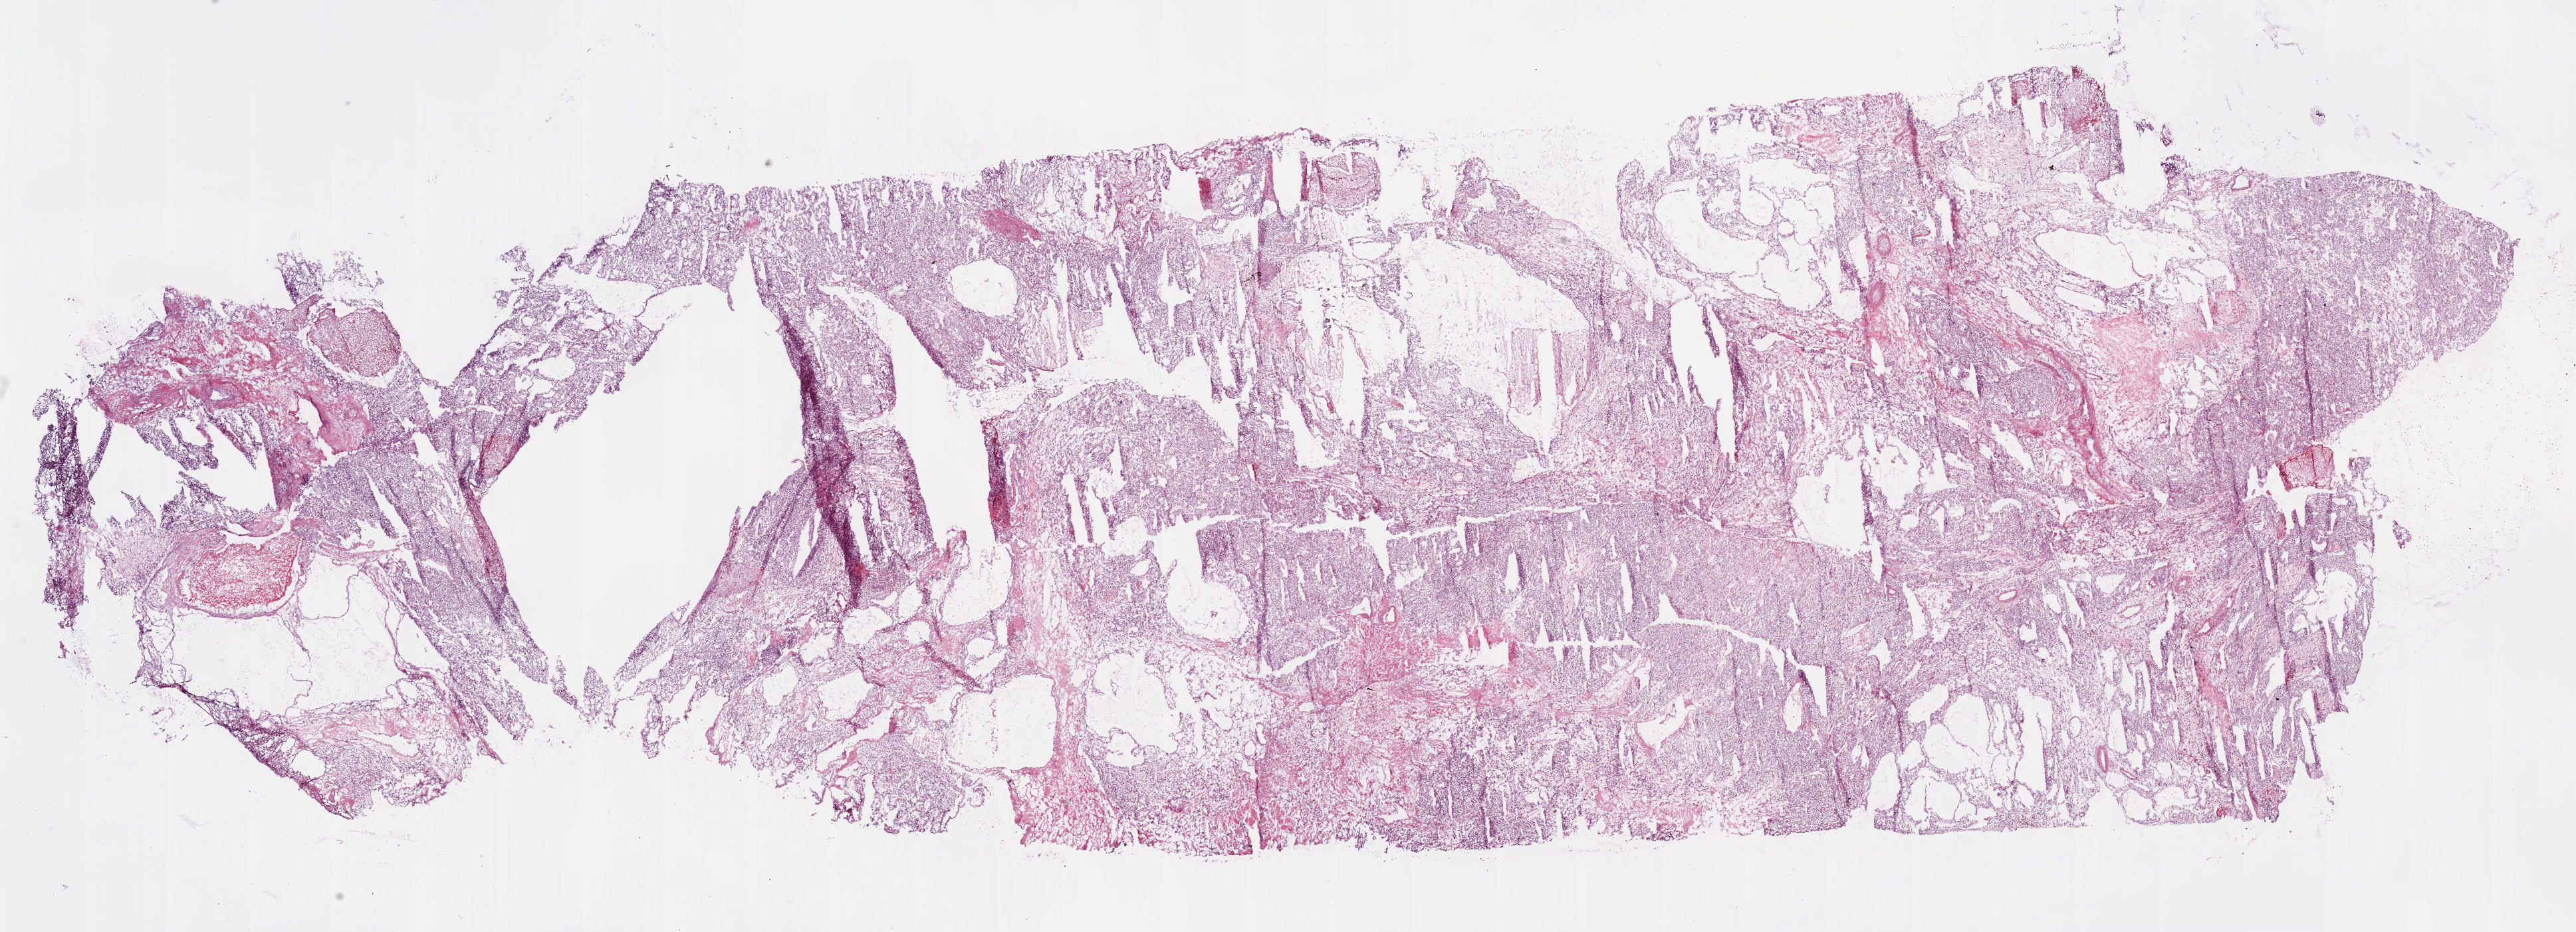
Digitized H&E-stained tissue section (whole slide) — whole scanned area (about 31.1 x 11.3 mm) shown as a low-resolution overview; frozen section; primary tumour sample from the kidney. Patient: male, age at initial diagnosis 47 years. Histologic grade: G2 (moderately differentiated). Pathologist review of this section (percent, as recorded): tumour cells 90%, tumour nuclei 85%, normal cells 0%, stromal cells 10%, necrosis 0%.
AJCC pathologic stage: II. TNM: T2 NX M0. Laterality: right. Diagnosis: Clear cell adenocarcinoma, NOS.